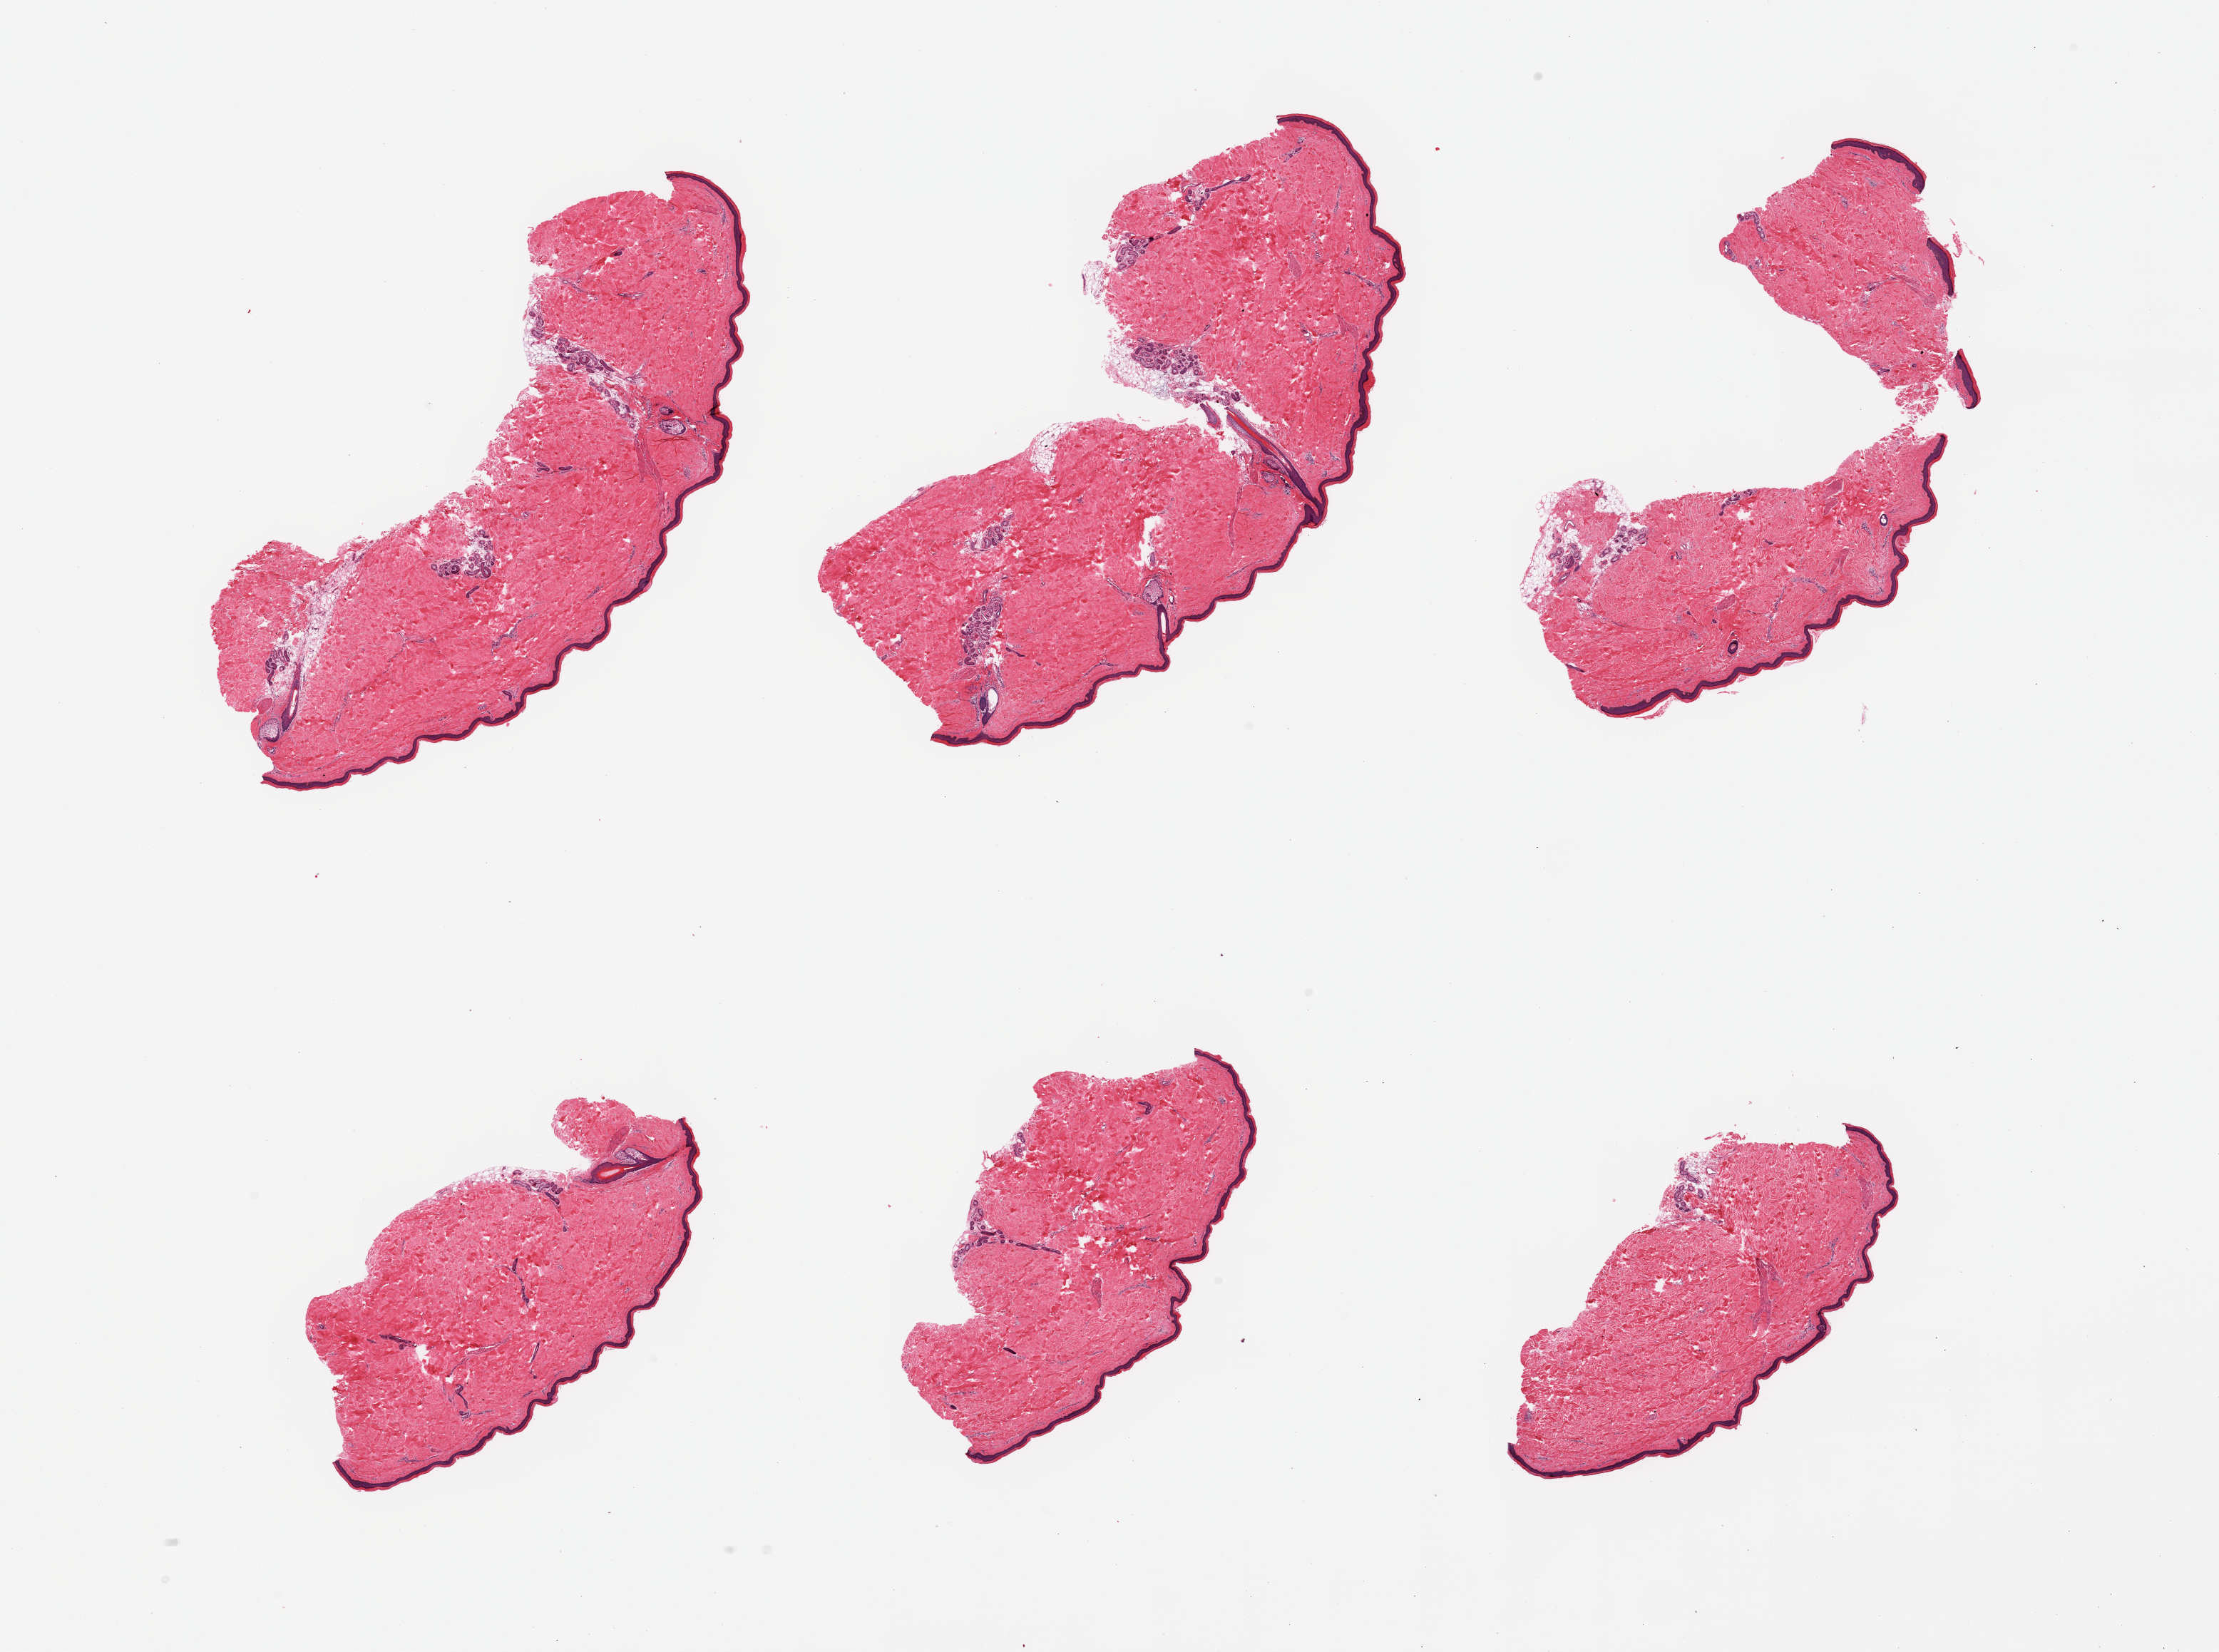
Whole-slide image, hematoxylin and eosin (H&E) stain, shown as a low-resolution overview of the whole scanned area (about 24.6 x 18.3 mm); PAXgene-fixed paraffin-embedded (PFPE) section; sampled site (target tissue): skin of lower leg; tissue donor sample.
Pathologist's review note for this sample: 6 pieces; well dissected; <2% dermal fat.